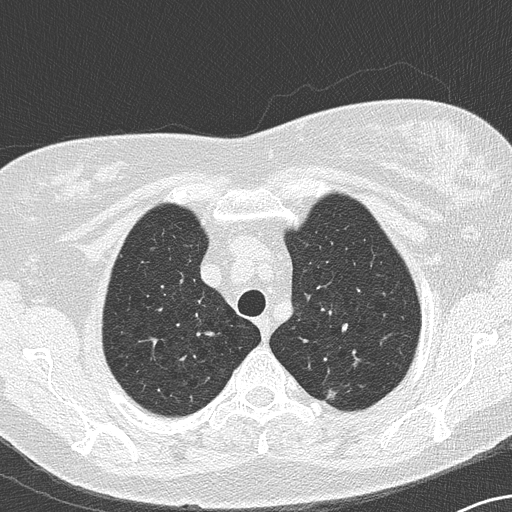
Chest CT (low-dose screening protocol), one axial image. Second screening round (one year after baseline). Lung window (W 1500 / L -600 HU). Slice 35 of 164 in the series. Female participant, aged 65 years at enrolment. Former smoker at enrolment.
Lesion marked by an expert reader, bounding box <312,380,355,413> (left, top, right, bottom; pixels). The exam's reader record, not a measurement of the box and not confirmed to be the same lesion: non-calcified nodule or mass ≥4 mm, left upper lobe, 7 × 6 mm, soft tissue attenuation, pre-existing on the prior screen: yes. Participant outcome: lung cancer diagnosed 428 days after this screen (after the third annual screen) — adenocarcinoma, NOS, left upper lobe, moderately differentiated (G2), stage IA (AJCC 6th edition), 8 mm at pathology.